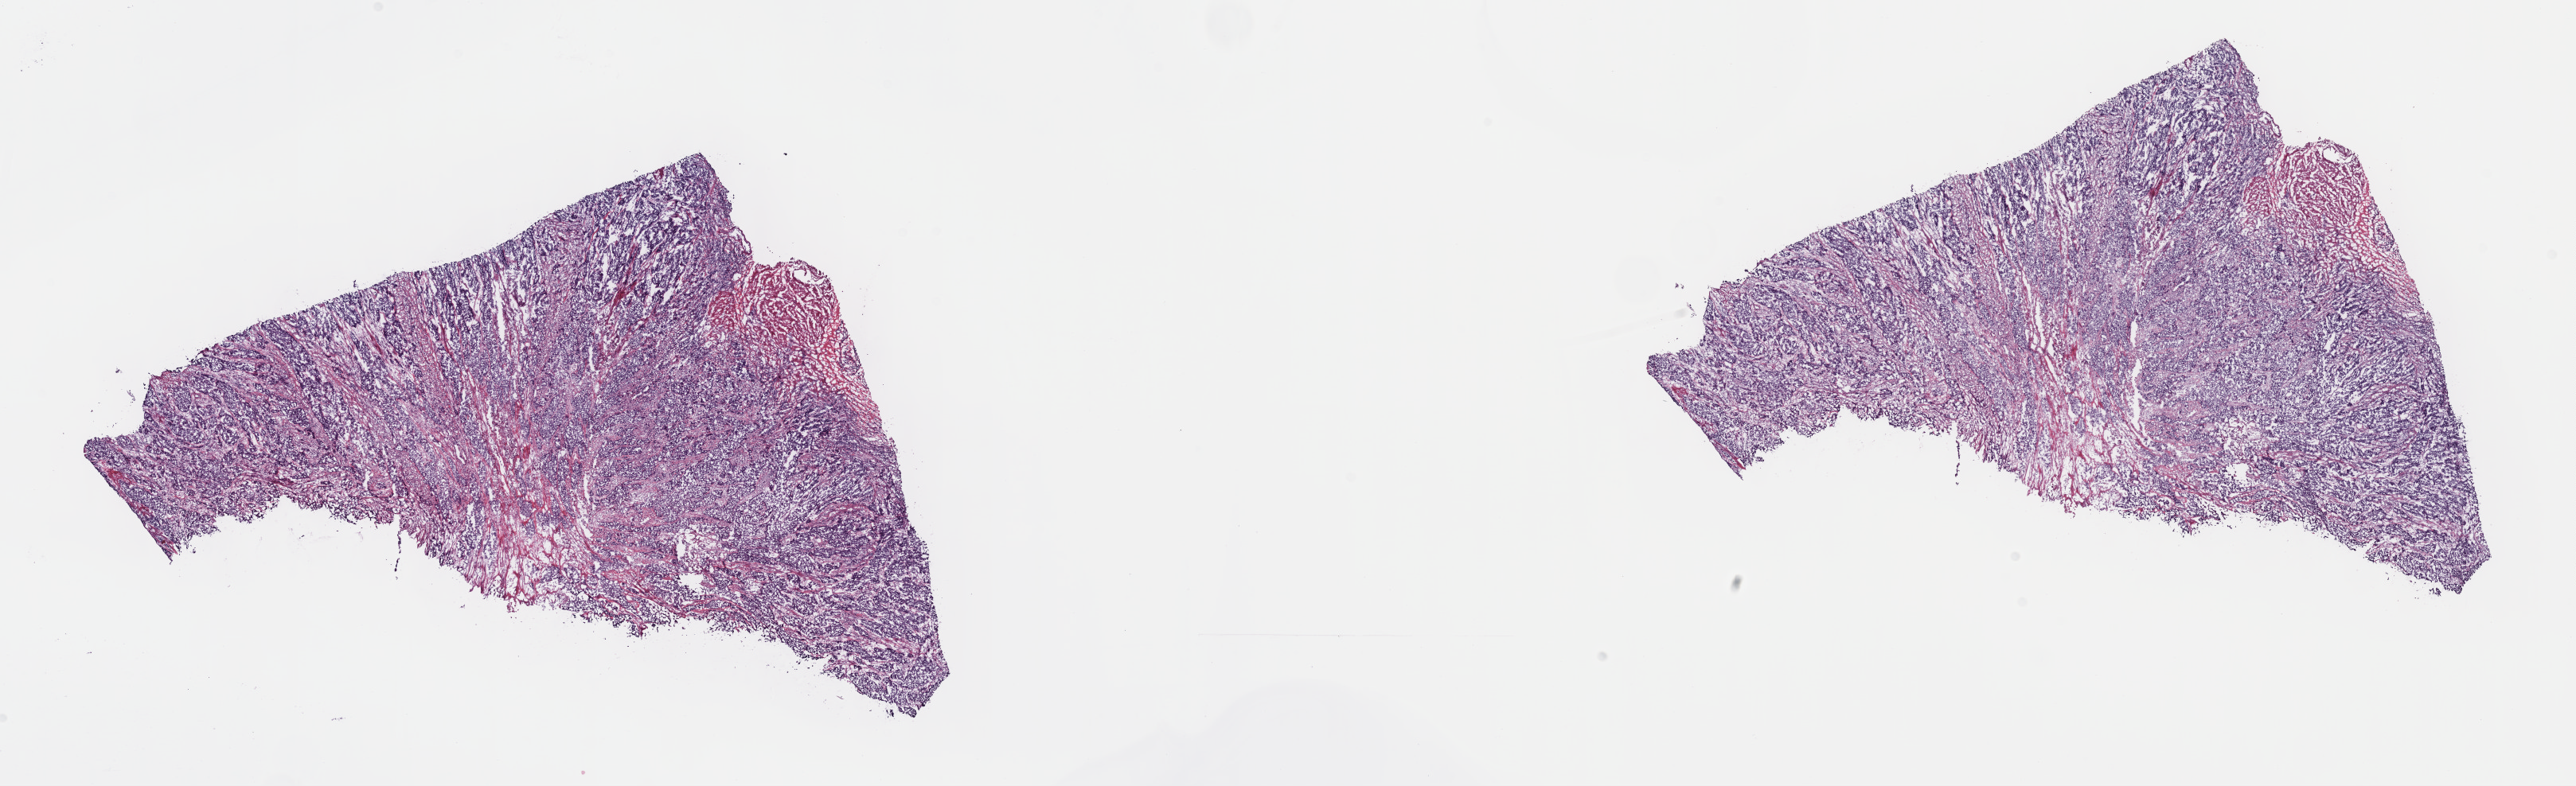
Whole-slide histology image, H&E, whole scanned area (about 26.2 x 8.0 mm) shown as a low-resolution overview. Frozen section from the top of the tissue portion. Bladder, primary tumour sample. Male, age 80 years at initial diagnosis. Histologic grade: high grade. Slide review estimates, as recorded: tumour cells 75%, tumour nuclei 75%, normal cells 0%, stromal cells 25%, necrosis 0%. Infiltration values recorded for this section: lymphocyte infiltration 2%, monocyte infiltration 1%, neutrophil infiltration 5%.
AJCC pathologic stage: III. TNM: T3a N0 MX. Diagnosis: Transitional cell carcinoma (anterior wall of bladder).